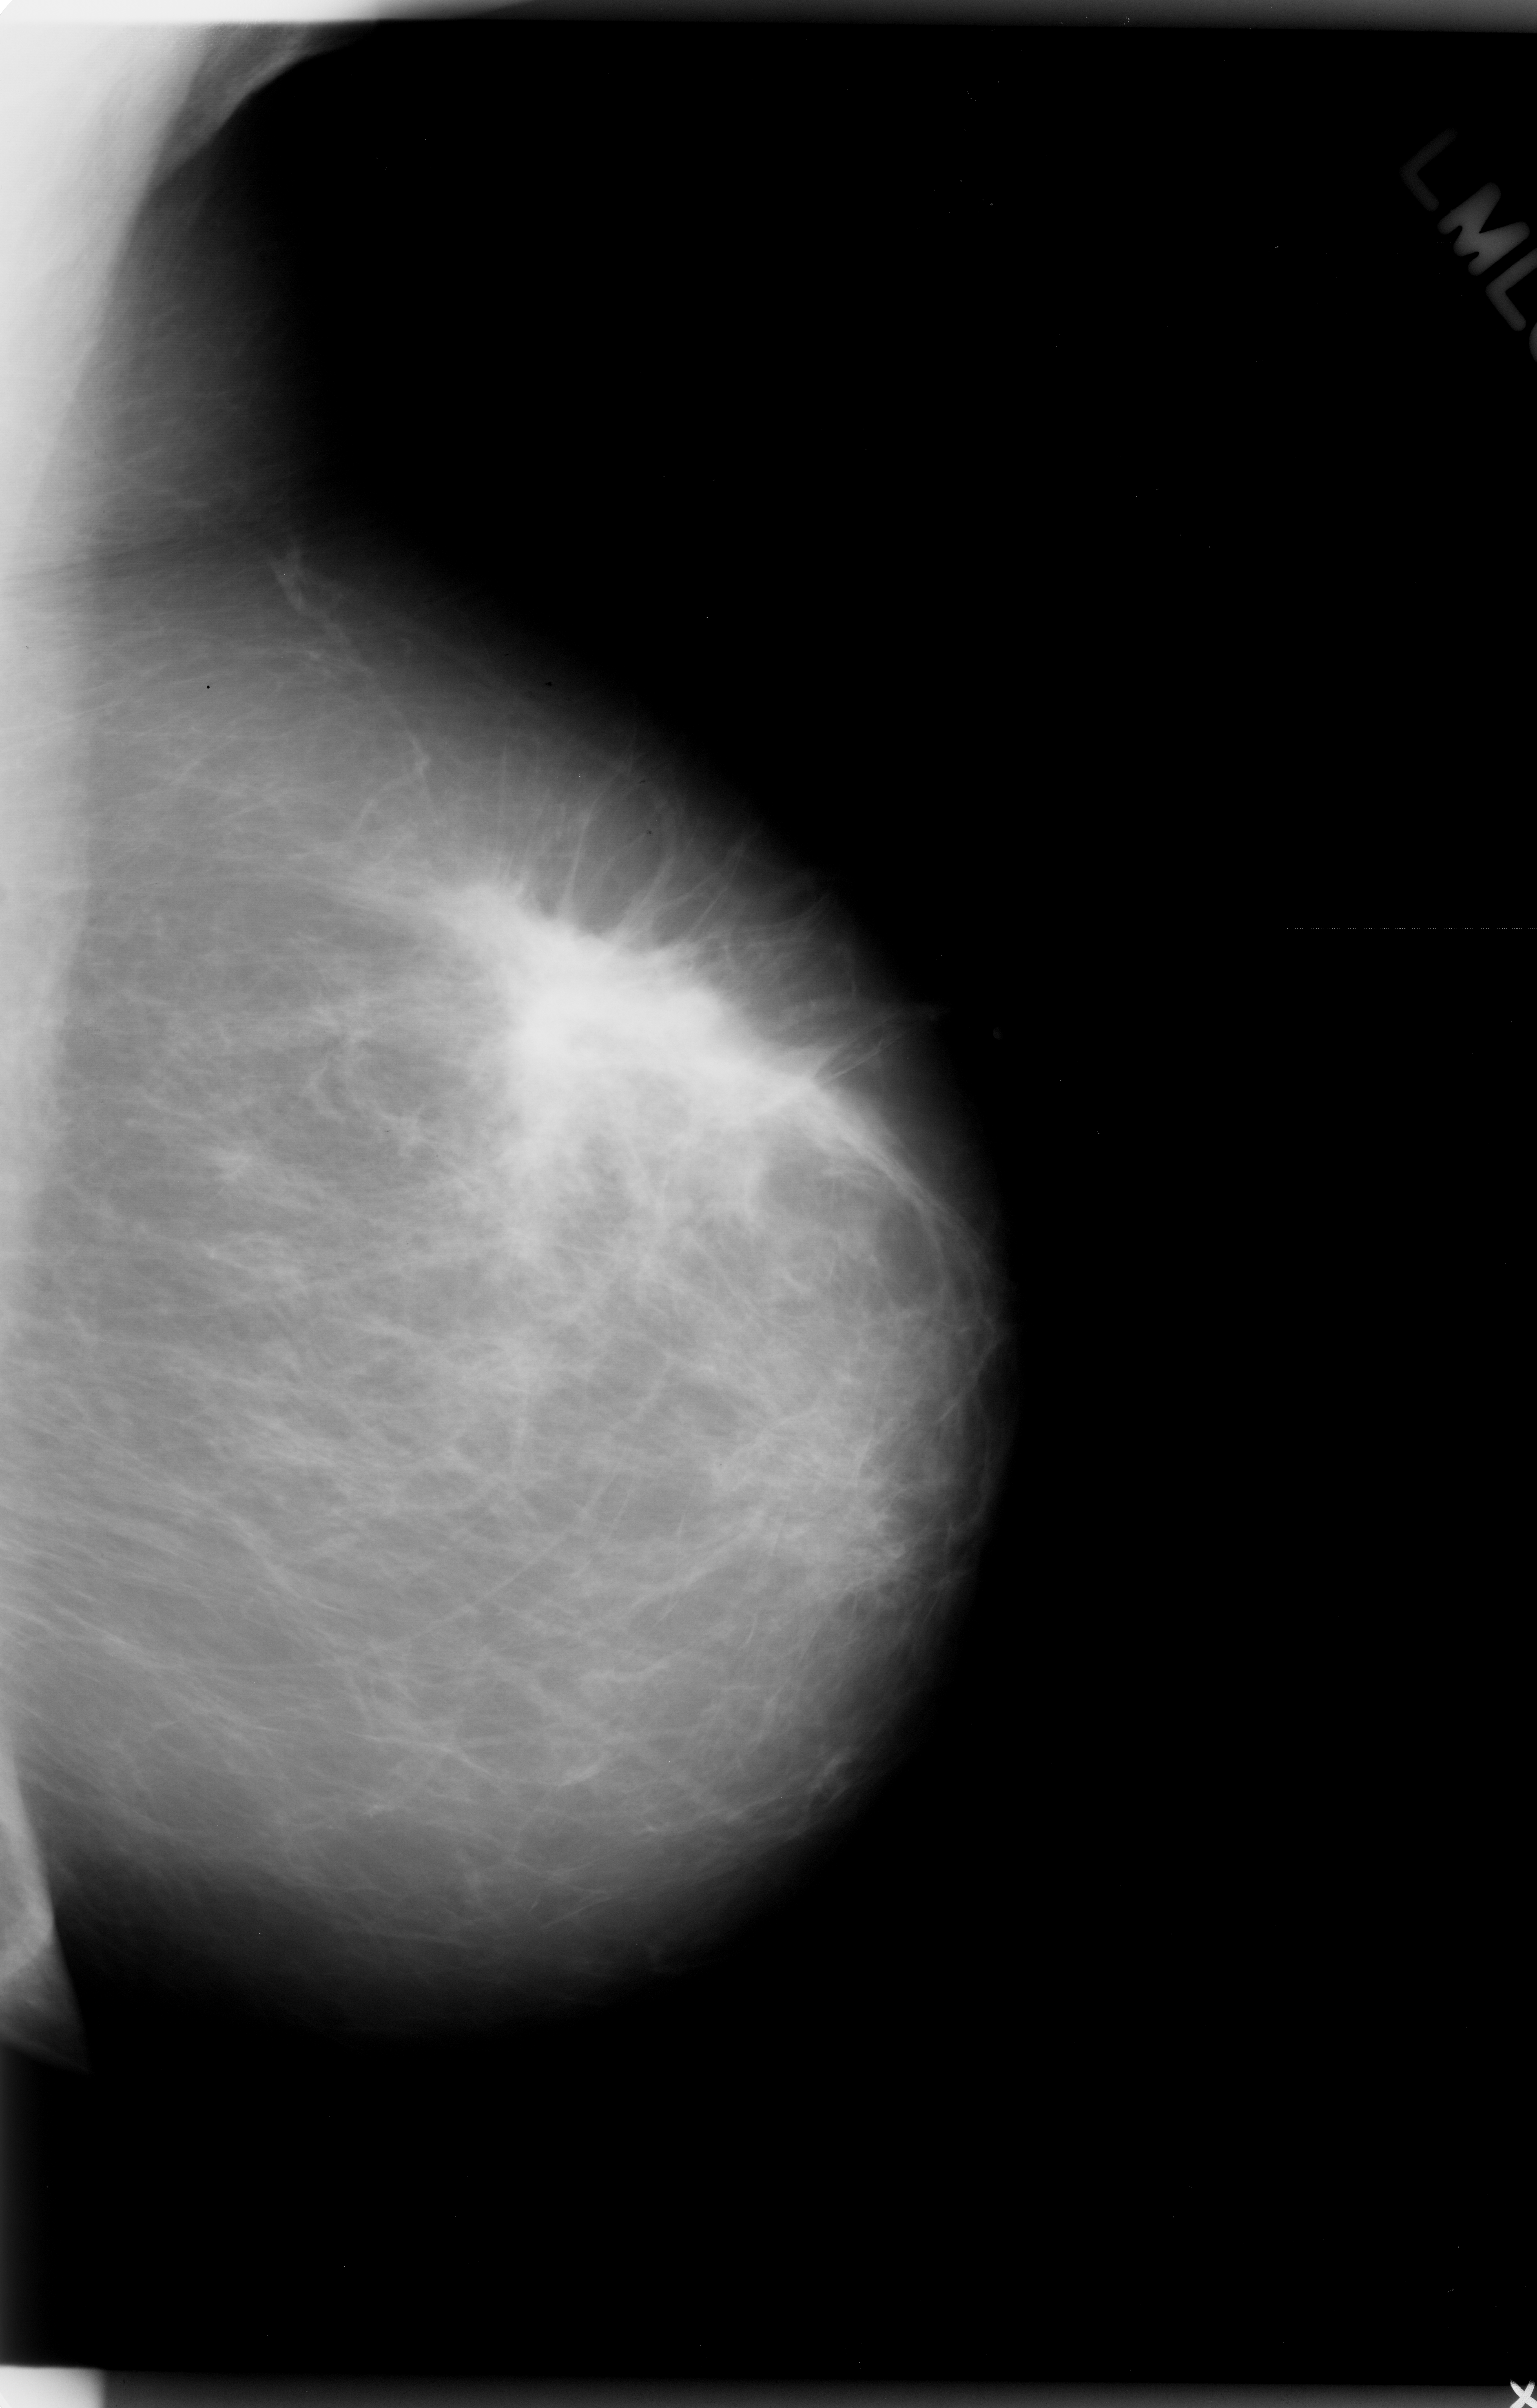
Scanned film-screen mammogram. Left breast. Mediolateral oblique (MLO) view. Breast composition: almost entirely fatty (BI-RADS density category 1 of 4). 1537 × 2408 image matrix.
Expert-marked regions of interest on this film, with their recorded descriptors:
- mass, shape irregular, margins spiculated; BI-RADS assessment category 5; pathology result (as recorded, not read from the image): malignant: bounding box (x1, y1, x2, y2) in pixels: (435, 885, 775, 1161)